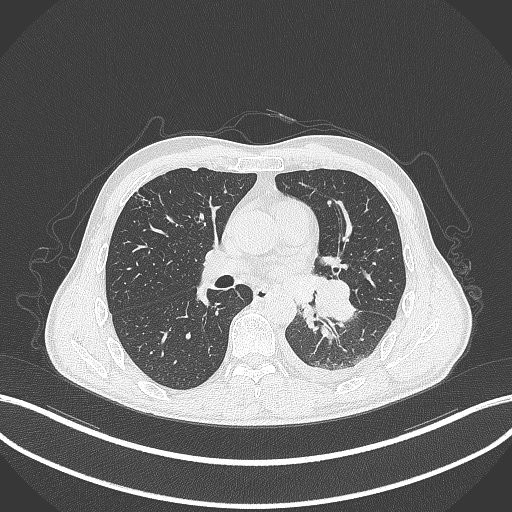
Chest CT, one axial slice. Position 170 of 295 along the scan axis. Reconstruction kernel B70f. 120 kVp. Lung window (W 1500 / L -600 HU). 1 mm slice thickness. 512 × 512 image matrix, field of view 400 × 400 mm. Male patient, age 47 years. Case-level facts recorded for this patient, not image findings: clinical TNM (as recorded): T3 N1 M1c; histopathological grade: G3.
Outlined on this slice (rectangle marked by the reading radiologist):
- lung tumour (recorded histology: small cell carcinoma): bounding box <309,276,362,323> (left, top, right, bottom; pixels)